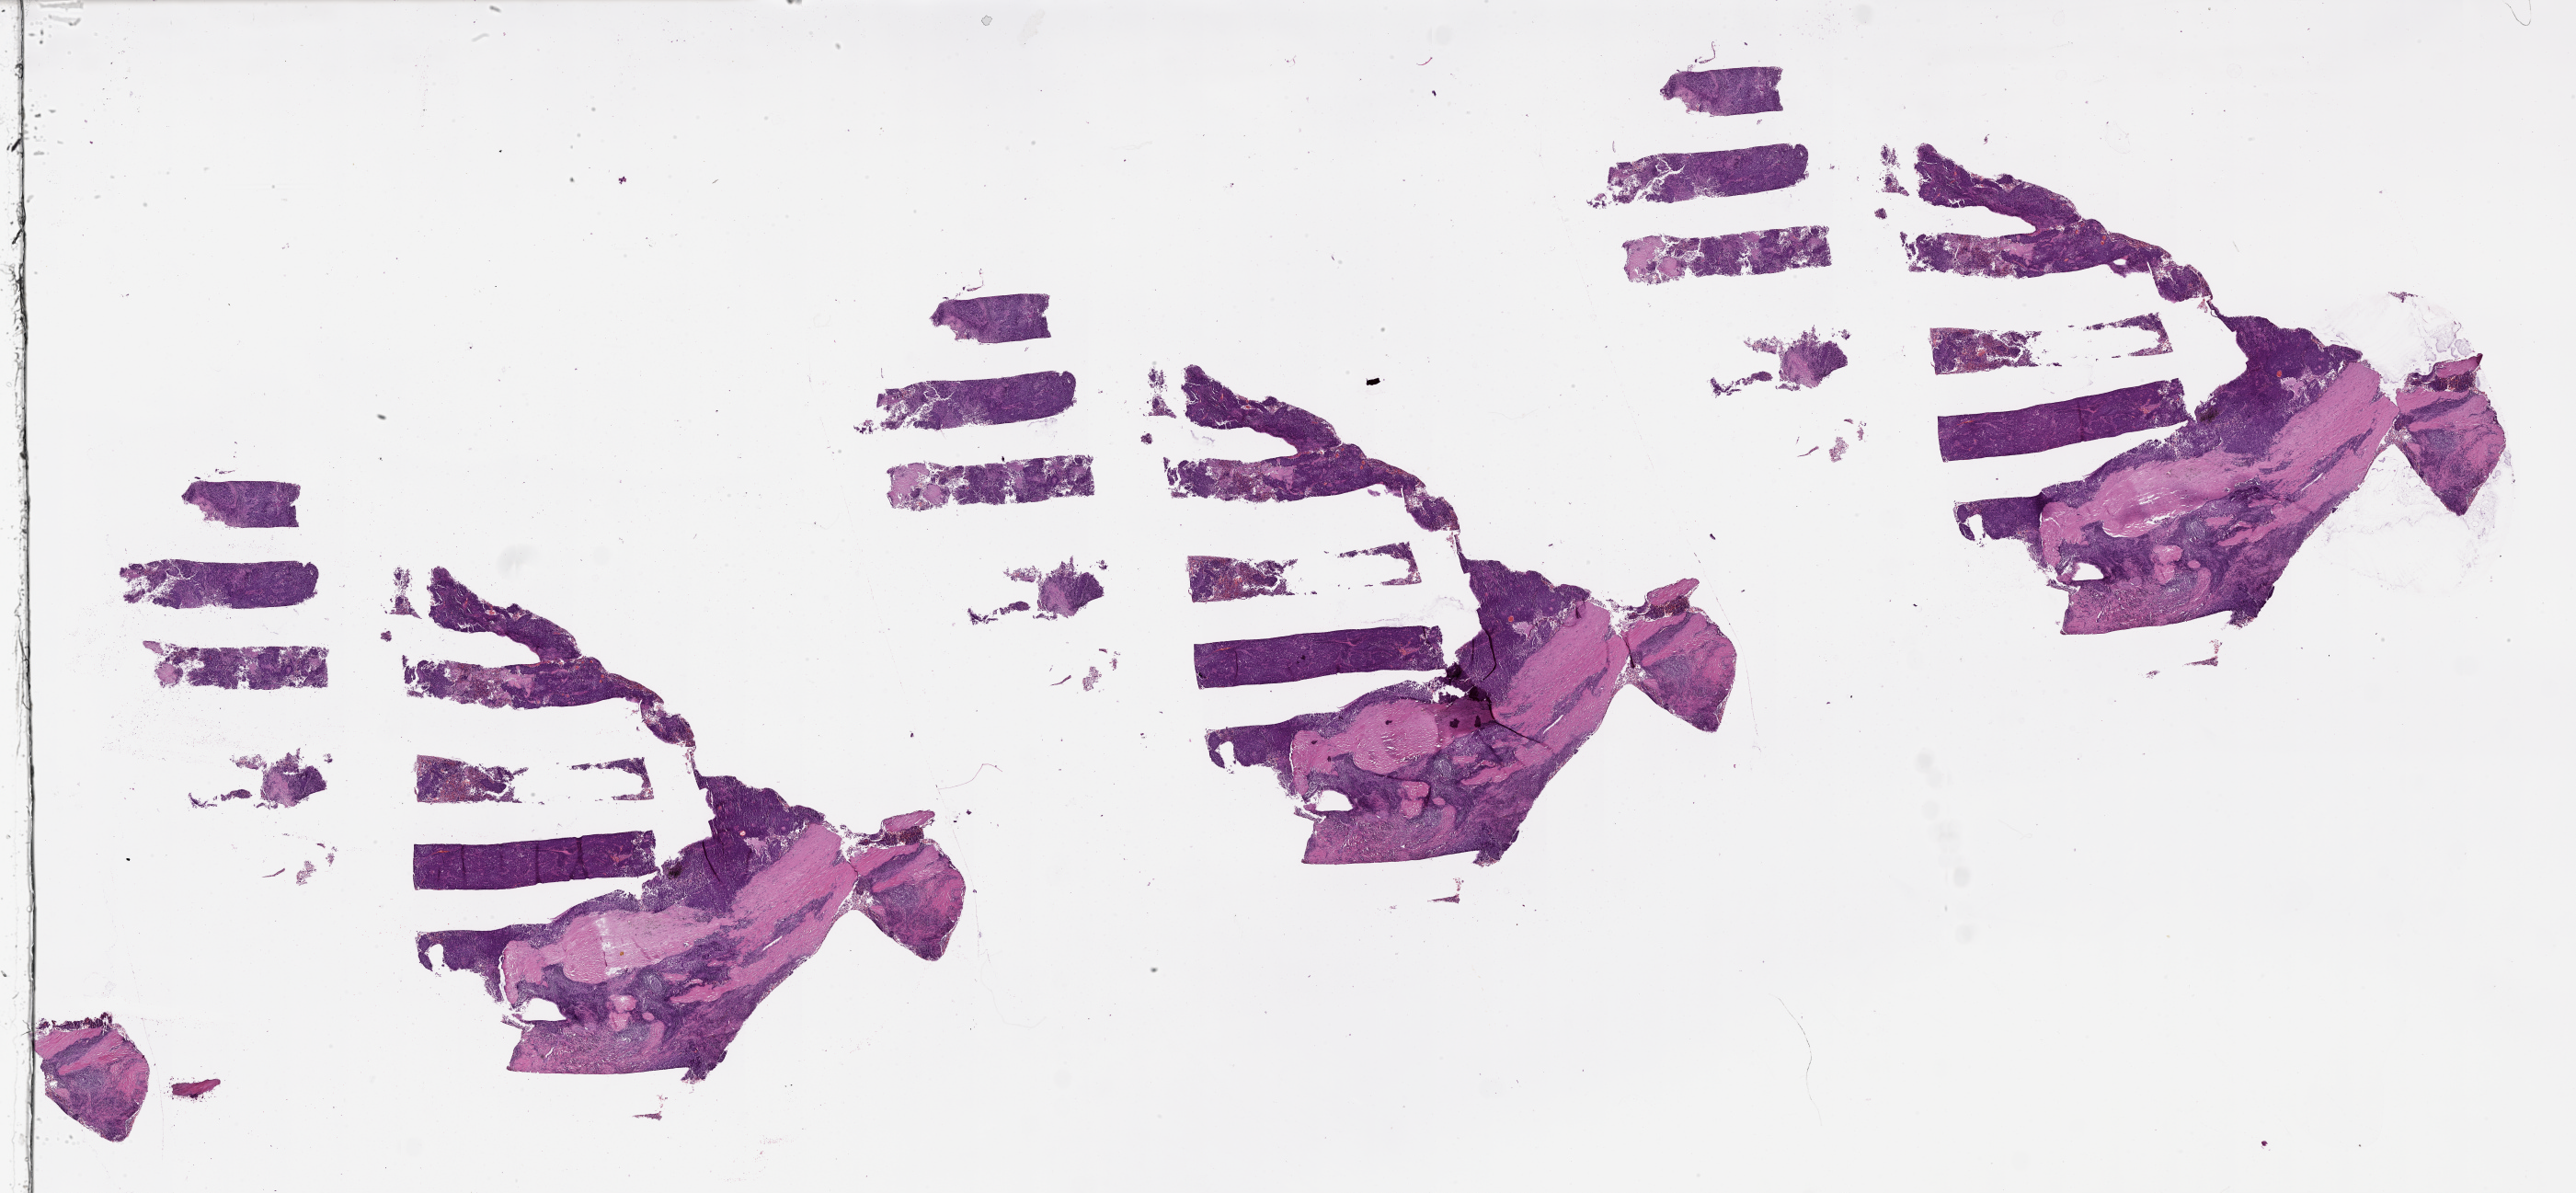
Whole-slide histology image, Hematoxylin and eosin (H&E) stained, low-resolution overview of the scanned area, about 45.1 x 20.9 mm (from a 20x scan); tumour tissue sample, lung. Patient: male, age 53 years.
Patient diagnosis (cohort enrolment): squamous cell carcinoma (lung).